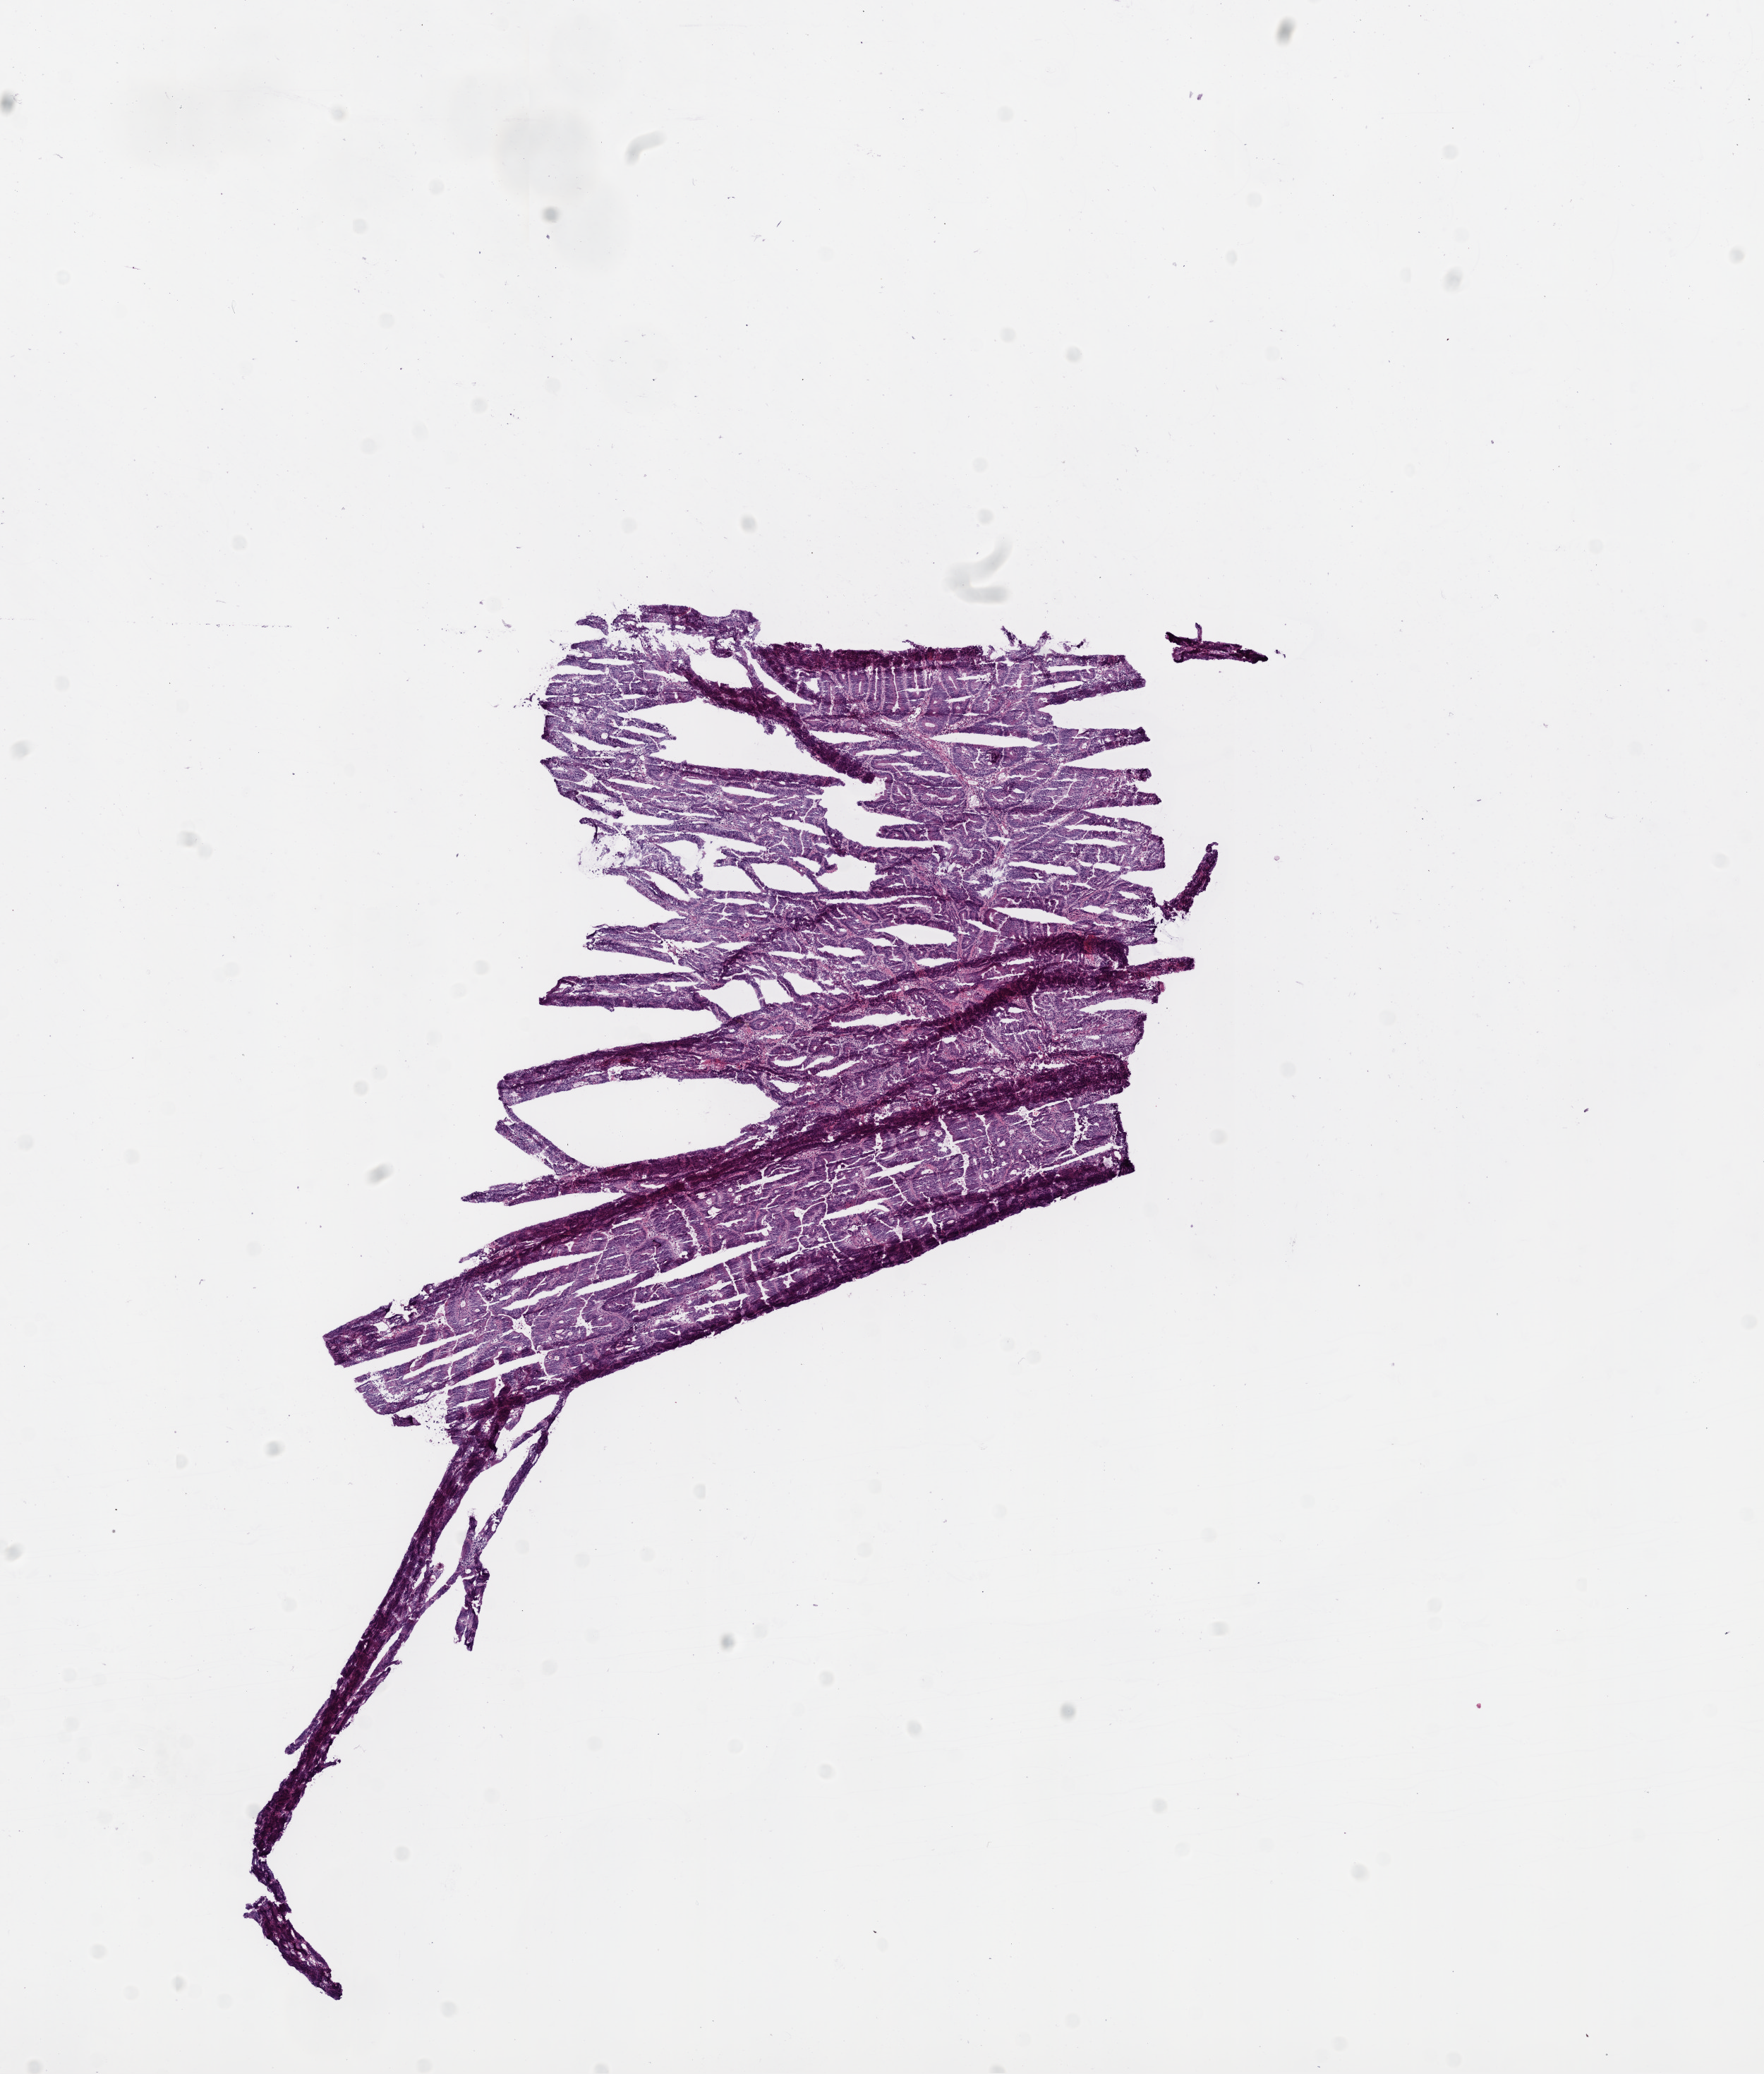
Whole-slide histology image, H&E-stained, shown as a low-resolution overview of the whole scanned area (about 10.0 x 11.8 mm). Frozen section from the top of the tissue portion. Rectum, primary tumour sample. Patient sex: female. Composition of this section per pathologist review: tumour cells 88%, tumour nuclei 70%, normal cells 0%, stromal cells 10%, necrosis 2%.
Lymph nodes positive (case pathology): 5 of 18 examined. AJCC pathologic stage: III. Diagnosis: Adenocarcinoma, NOS.